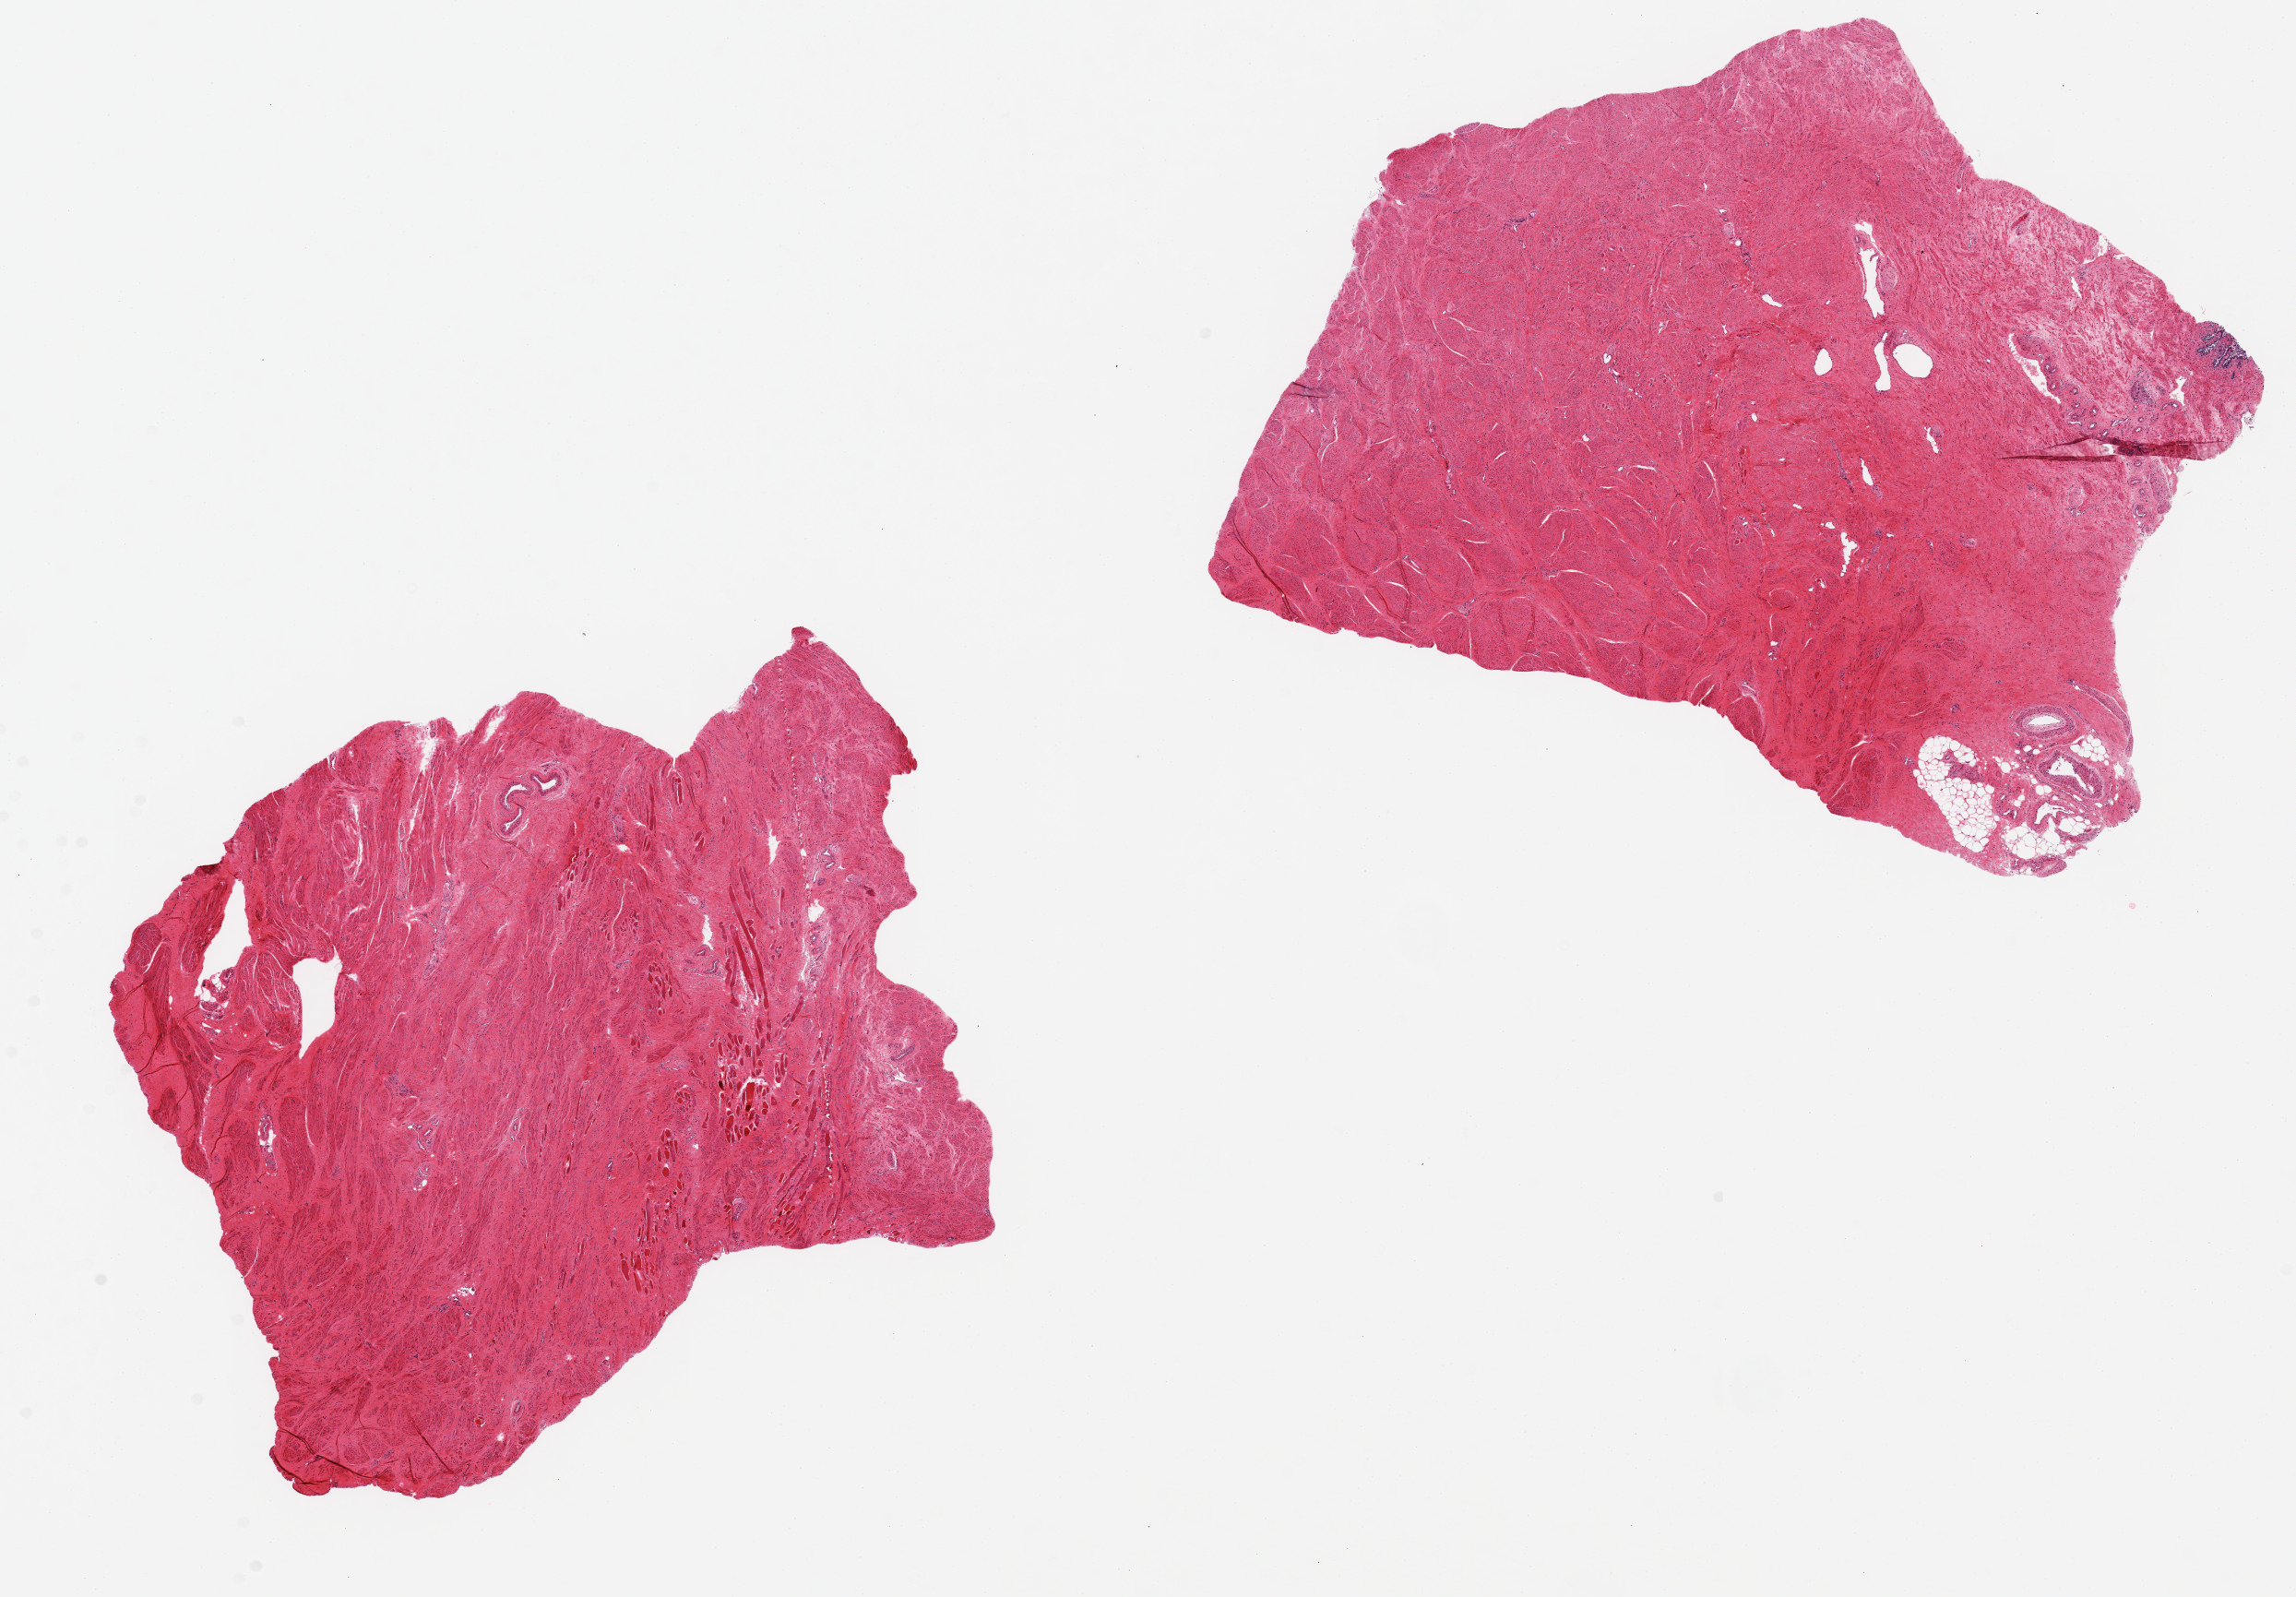
Digitized hematoxylin and eosin (H&E)-stained section, low-resolution overview of the scanned area, about 19.7 x 13.7 mm (from a 20x scan), PAXgene-fixed, paraffin-embedded tissue, target tissue: prostate, tissue donor sample. Donor sex: male.
Reviewer comment on this tissue sample: 2 pieces, 7x6 & 8x6.5mm; virtually all composed of fibromuscular tissue.